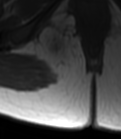
MRI of an extremity soft-tissue mass, one axial slice. Position 31 of 47 along the scan axis. MR volume resampled by the dataset authors to the PET/CT grid (not the native acquisition matrix). 3.27 mm slice thickness. 121 × 139 image matrix. Female patient. From the clinical record (not read from this slice): histological type: epithelioid sarcoma; grade: intermediate; site of the primary tumour: right buttock.
Structures marked on this image (expert contour drawn on MRI and transferred to this co-registered scan by the dataset authors):
- gross tumour volume including surrounding oedema: bounding box (x1, y1, x2, y2) in pixels: (38, 25, 78, 71)
- gross tumour volume (mass): (43, 32, 69, 62)